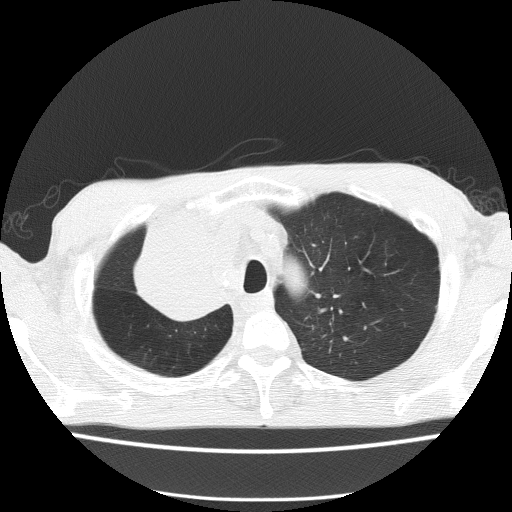
Chest CT (low-dose screening protocol), one axial image. First (baseline) screen. Lung window (W 1500 / L -600 HU). 2 mm slice thickness. Lung (sharp) reconstruction kernel (FC51). 120 kVp. Male participant, aged 59 years at enrolment. Former smoker at enrolment.
- Expert-annotated lung lesion, bounding box <129,235,241,327> (left, top, right, bottom; pixels).
- The screening reader recorded 5 non-calcified nodules or masses ≥4 mm on this exam (left upper lobe, left upper lobe, left upper lobe, right middle lobe, right lower lobe); which of them this box marks is not recorded.